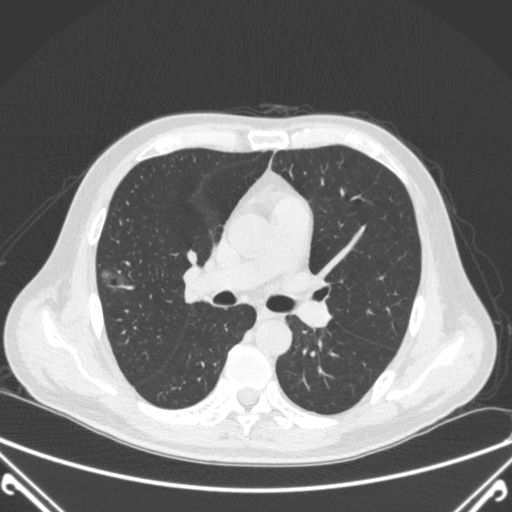
Chest CT, one axial slice. Position 220 of 360 along the scan axis. 120 kVp. Lung window (W 1500 / L -600 HU). 1 mm slice thickness. 512 × 512 image matrix, field of view 380 × 380 mm. Male patient, age 64 years. Case-level facts recorded for this patient, not image findings: clinical TNM (as recorded): T1c N0 M0.
Annotated regions visible in this slice (rectangle marked by the reading radiologist):
- lung tumour (recorded histology: adenocarcinoma): box from (x=91, y=263) to (x=131, y=299) px